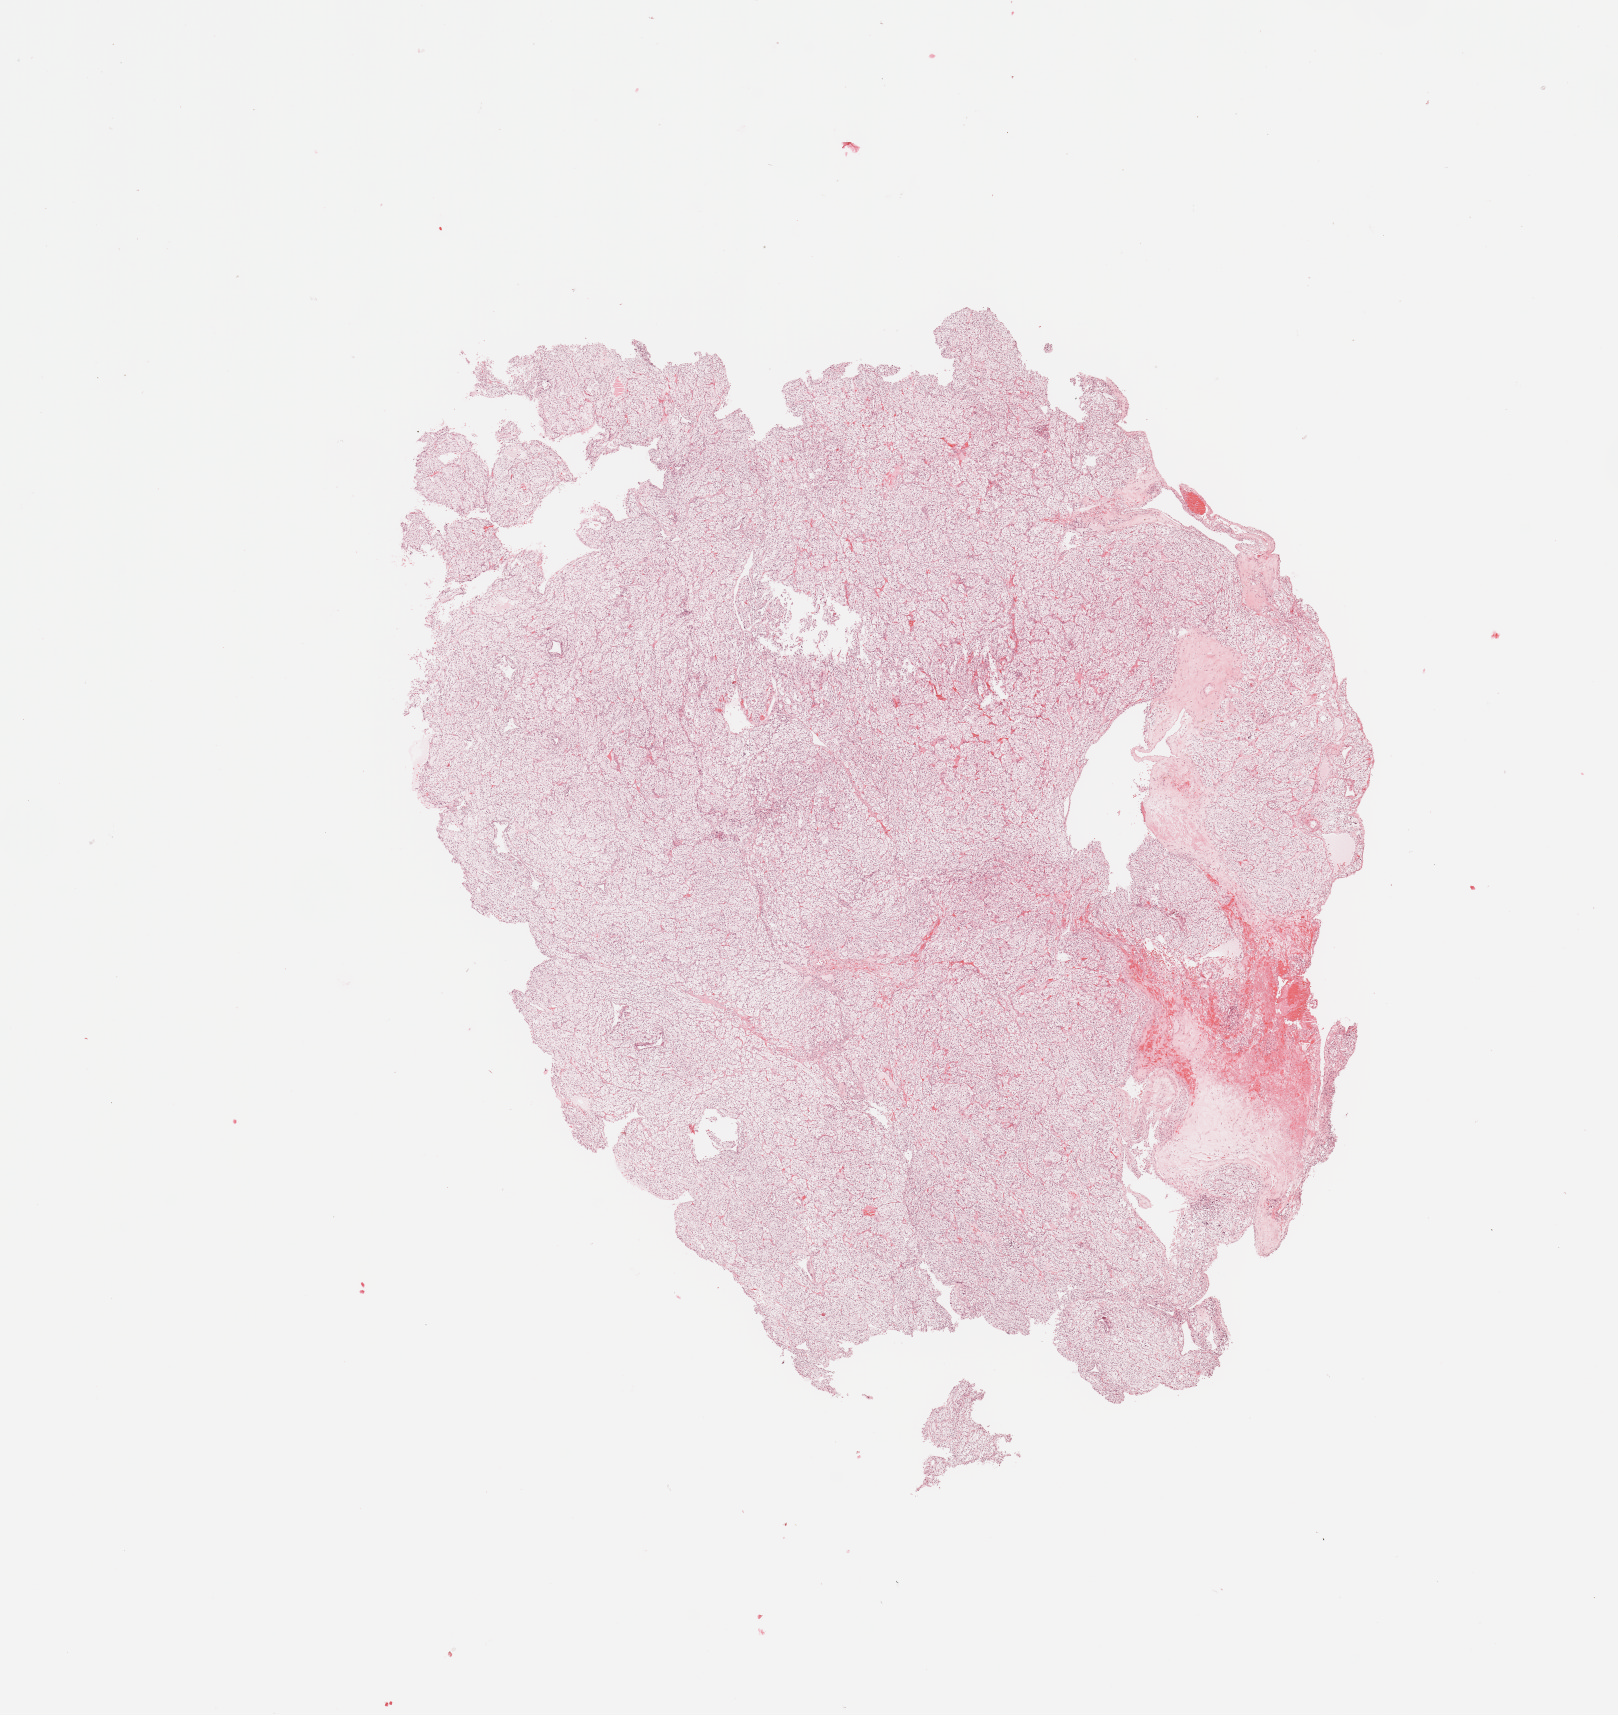
Digitized H&E-stained tissue section (whole slide), whole scanned area (about 12.8 x 13.6 mm, from a 20x scan) shown as a low-resolution overview; tumour tissue sample, sampled site: kidney. Male, 50 y/o. Histologic grade: G2 (moderately differentiated). Composition of this section per pathologist review: tumour nuclei 85%, necrosis 0%.
AJCC pathologic stage: II. Diagnosis: Renal cell carcinoma, NOS. Primary tumour site (as recorded): upper pole.